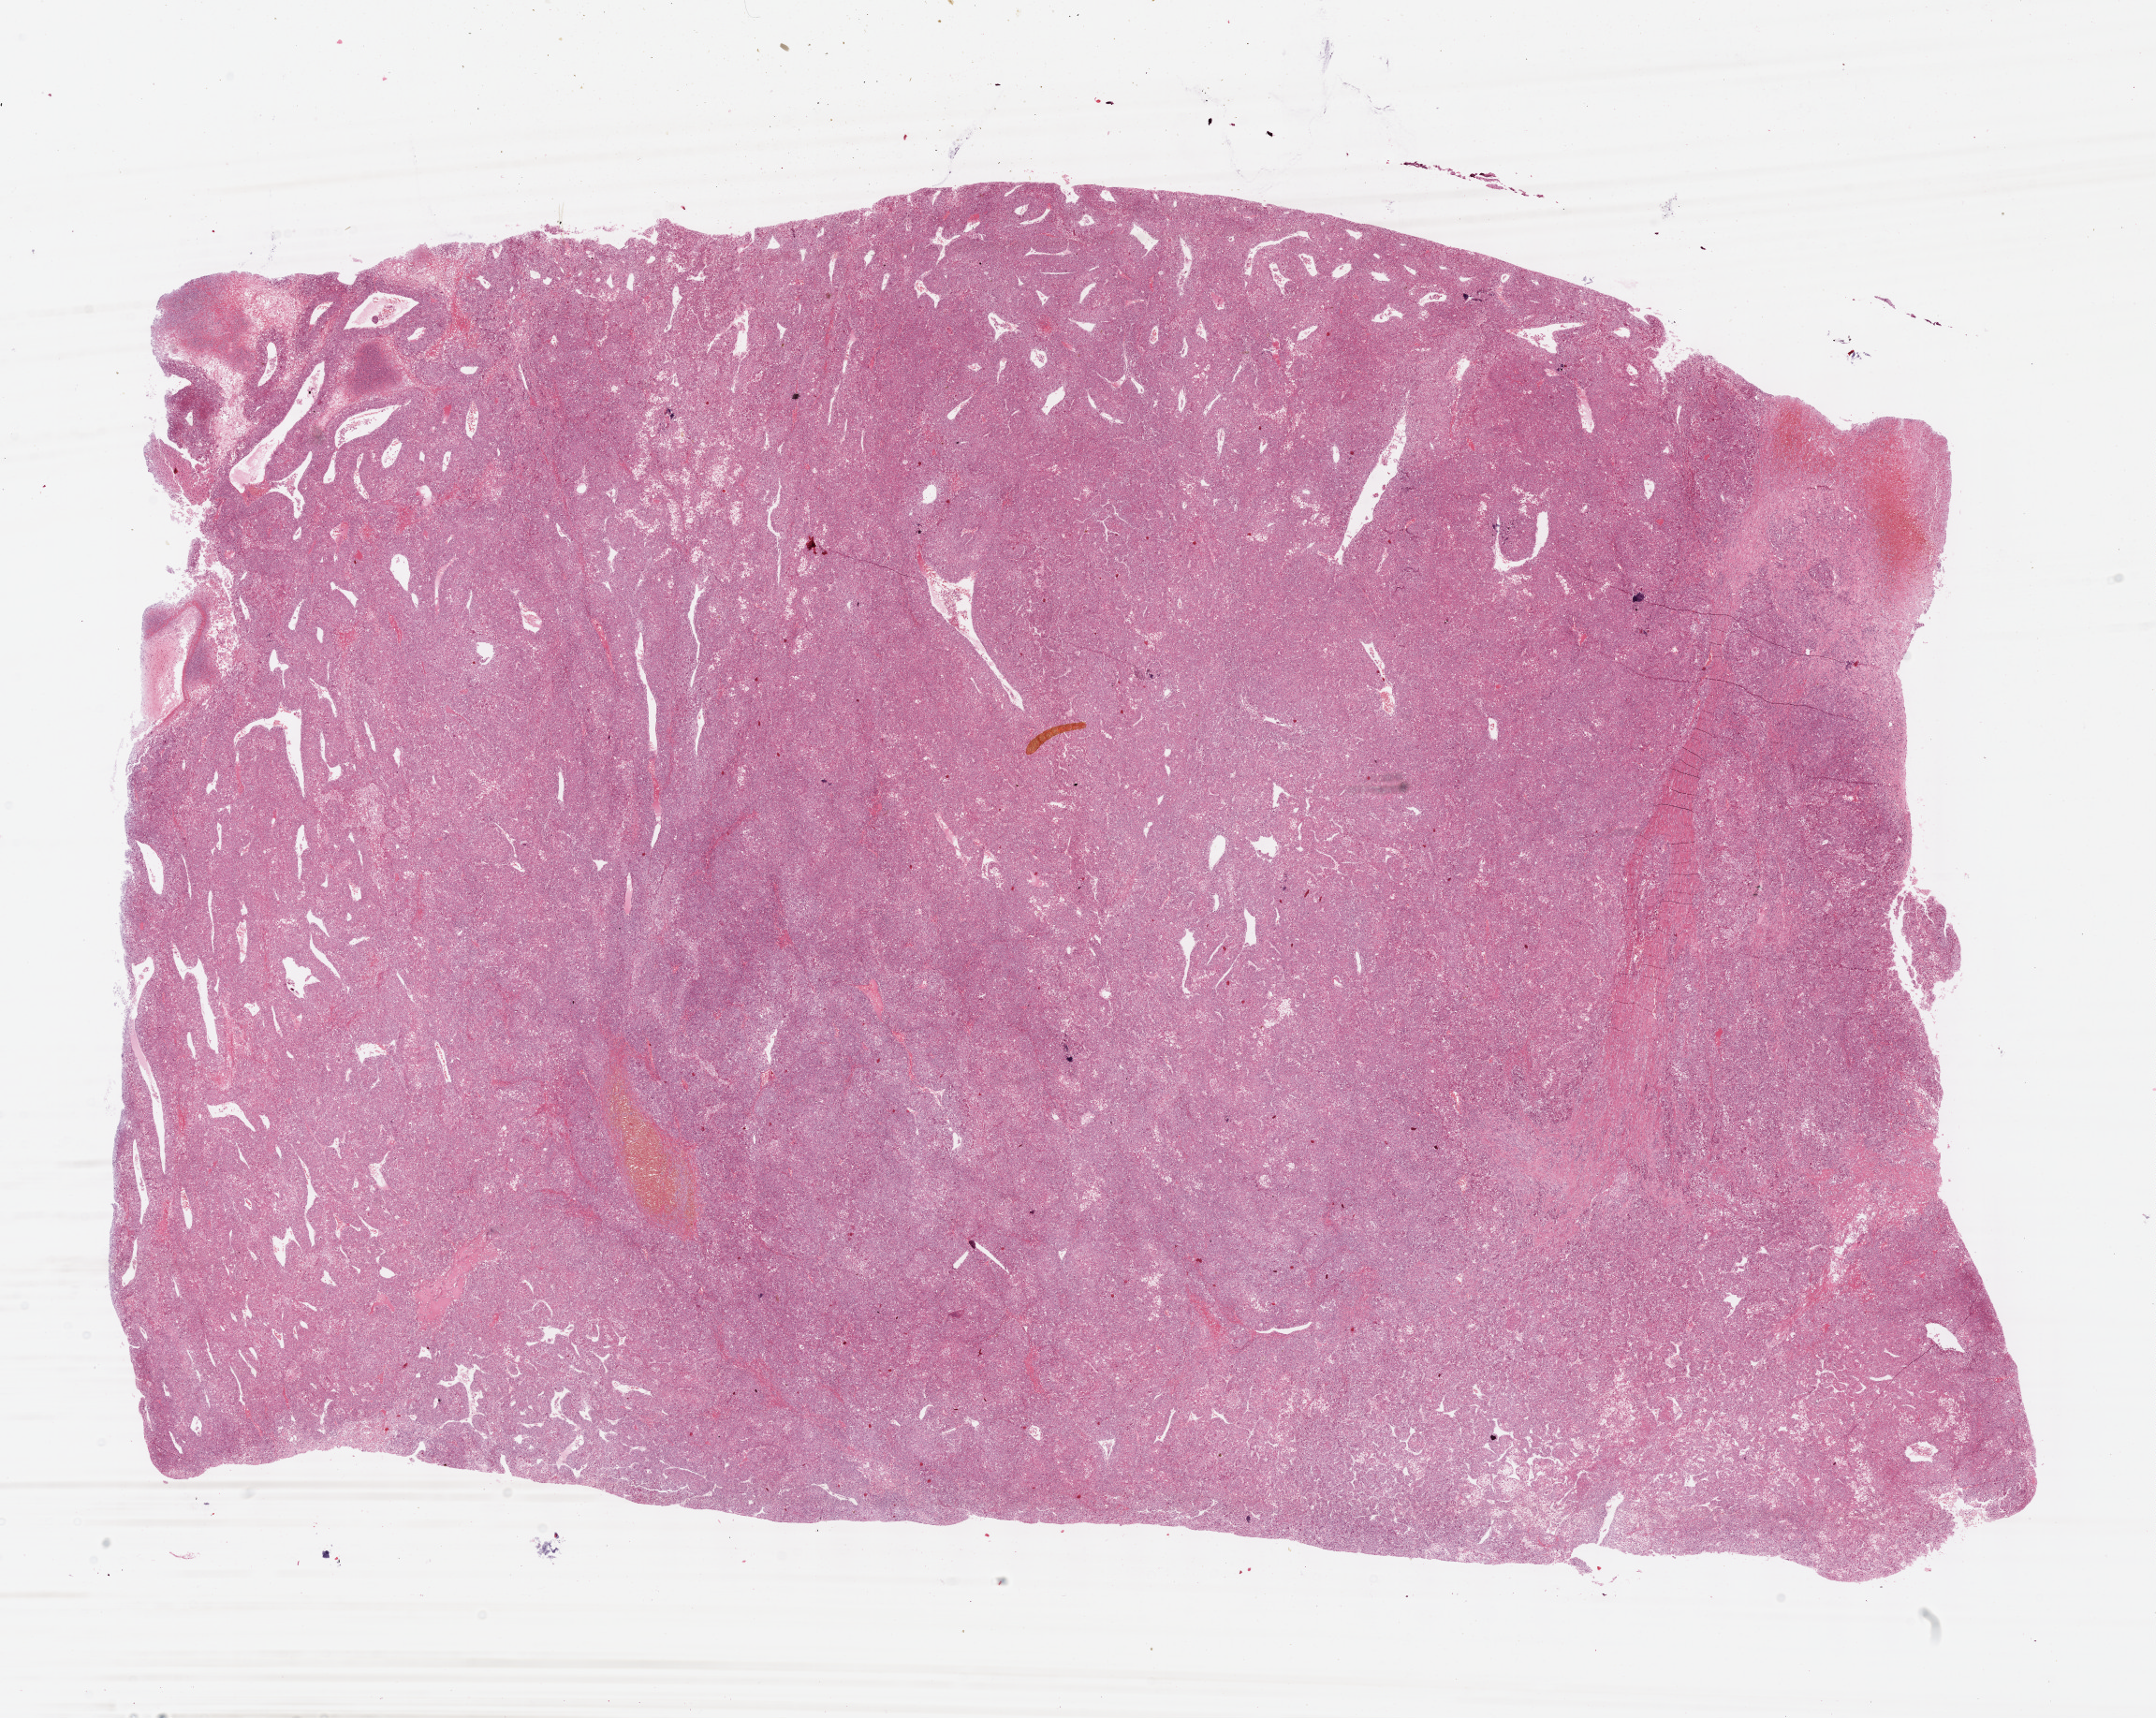
Digitized Hematoxylin and eosin (H&E) stained tissue section (whole slide) — shown as a low-resolution overview of the whole scanned area (about 18.6 x 14.8 mm). Formalin-fixed paraffin-embedded (FFPE) diagnostic section. Liver, primary tumour sample. Patient: male, age at initial diagnosis 74 years. Histologic grade: G2 (moderately differentiated).
* diagnosis: Hepatocellular carcinoma, NOS
* AJCC pathologic stage: IIIA